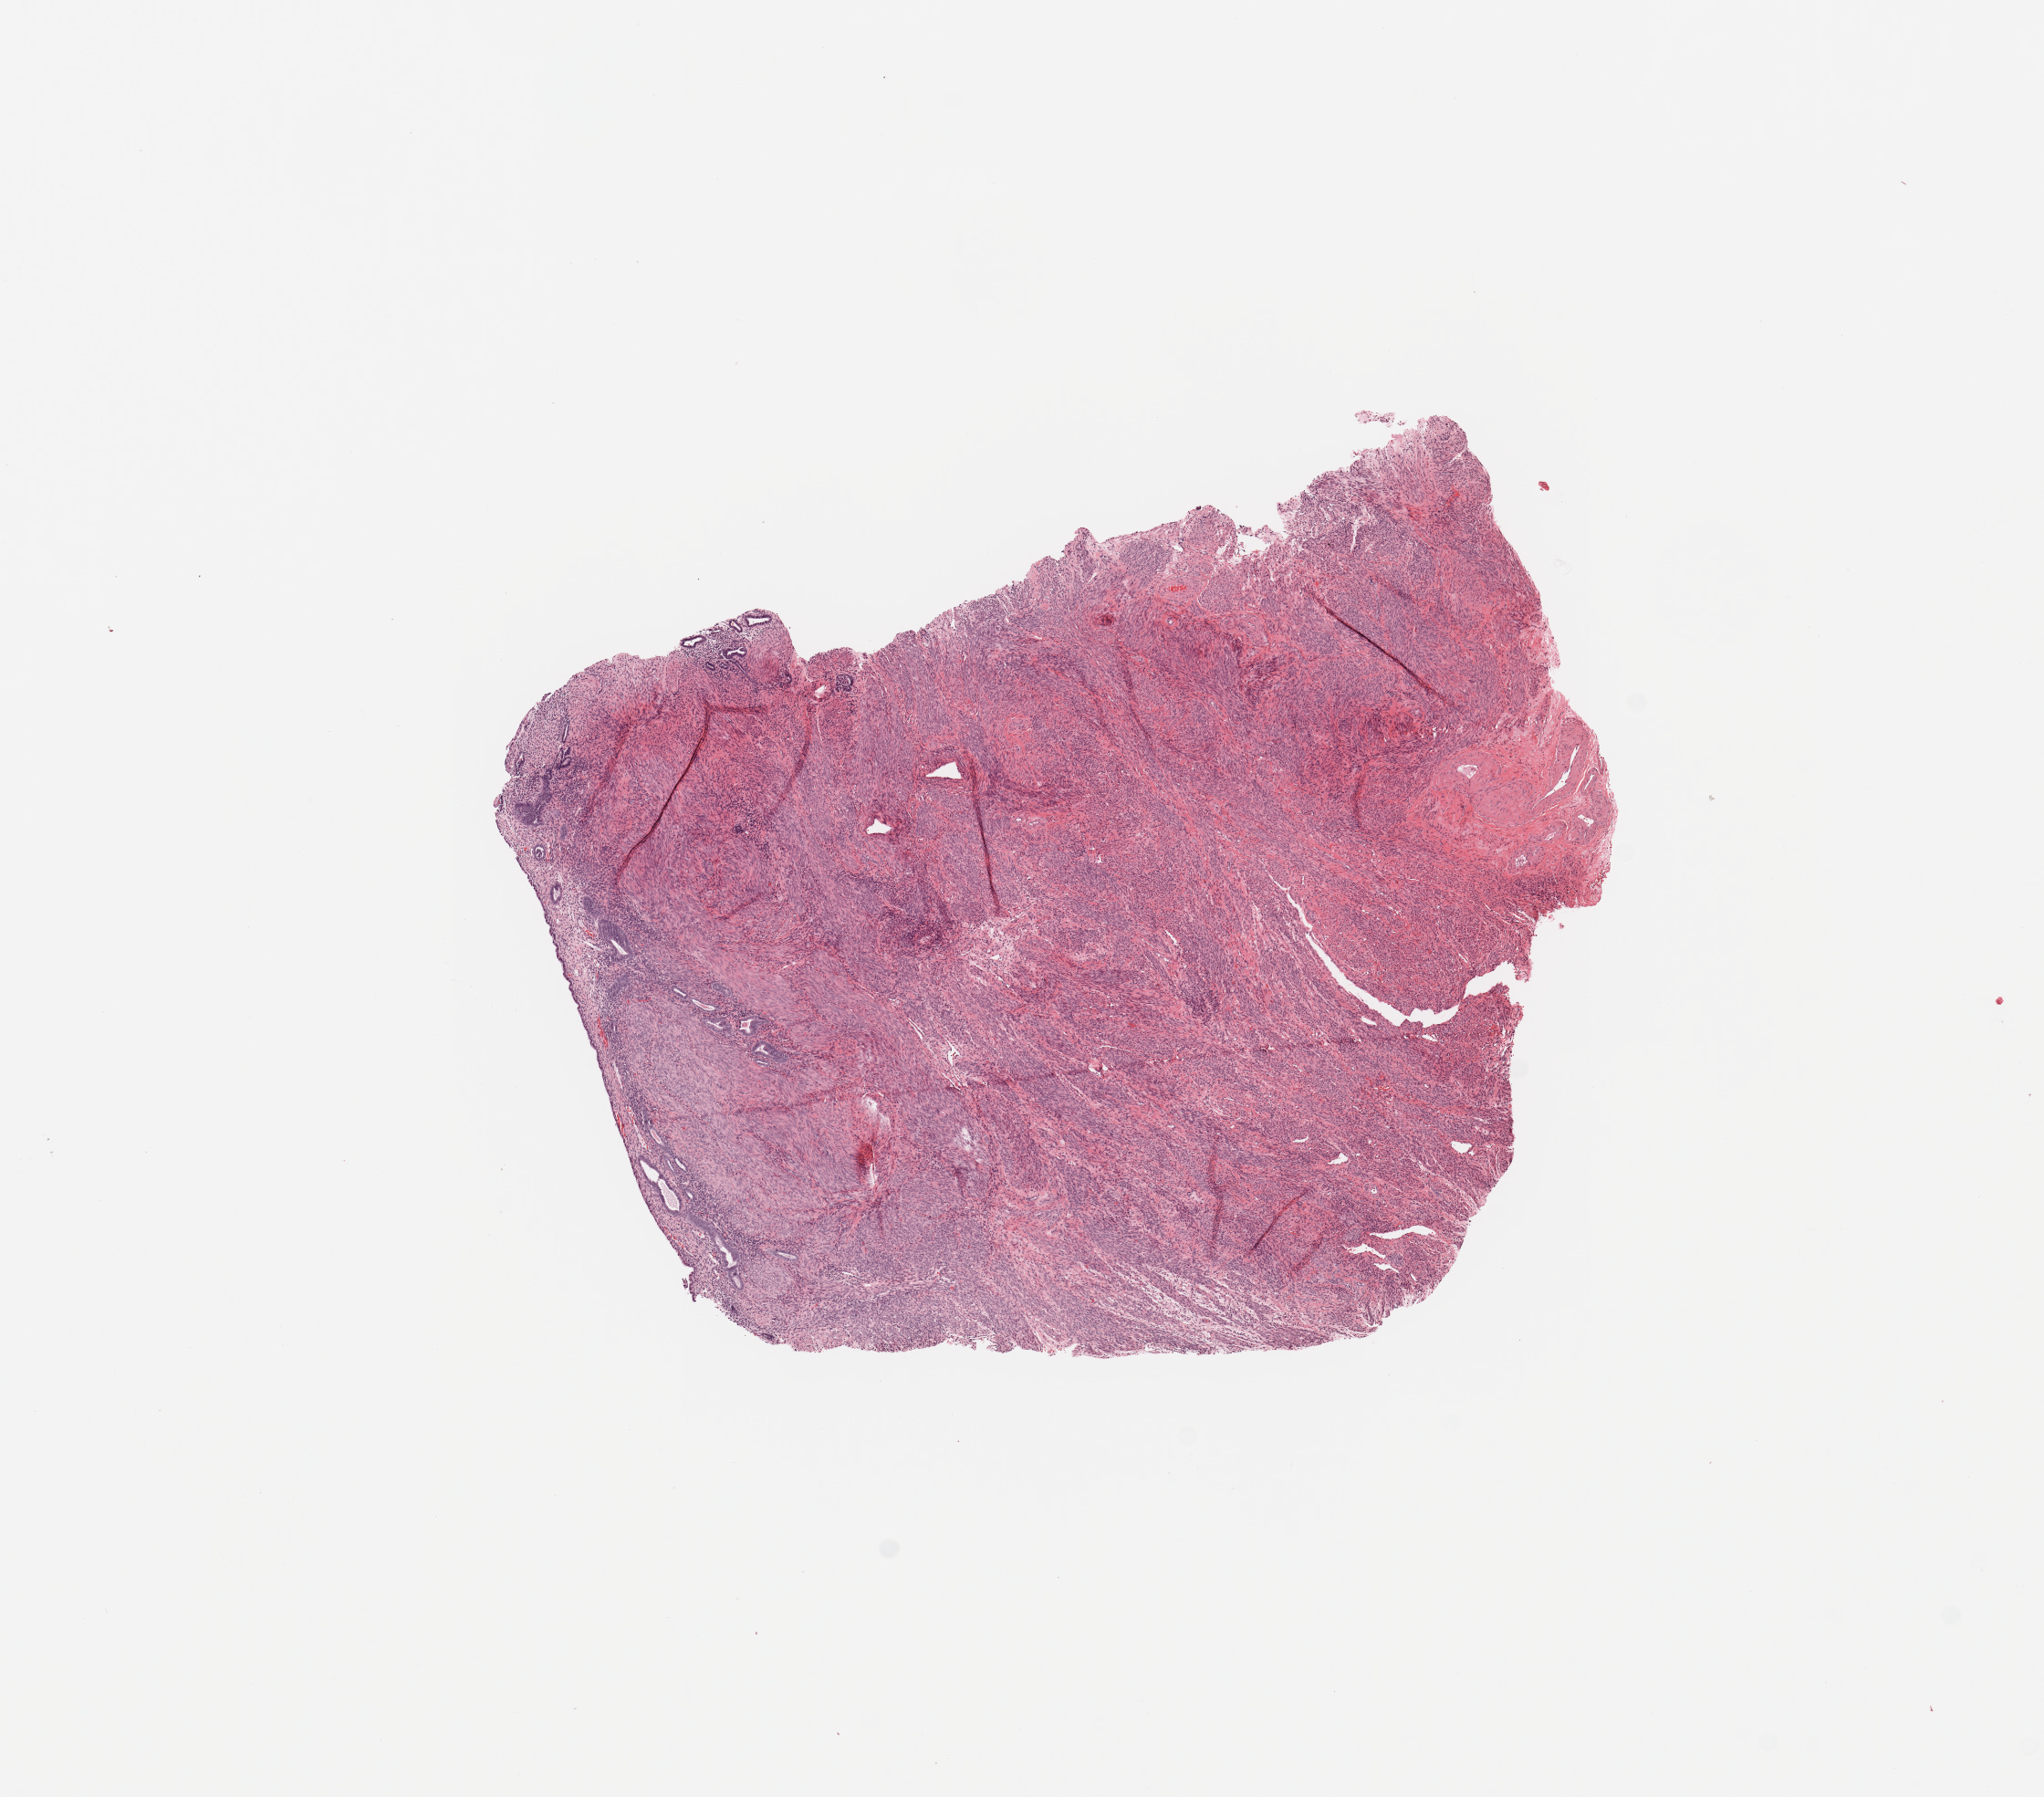
Whole-slide histology image, H&E-stained, whole scanned area (about 8.9 x 7.8 mm, acquisition: 20x scan) shown as a low-resolution overview; normal (non-tumour) tissue sample, uterus. Patient: female, age 65 years.
• this section: normal (non-tumour) tissue from the same patient
• patient diagnosis: Endometrioid adenocarcinoma, NOS